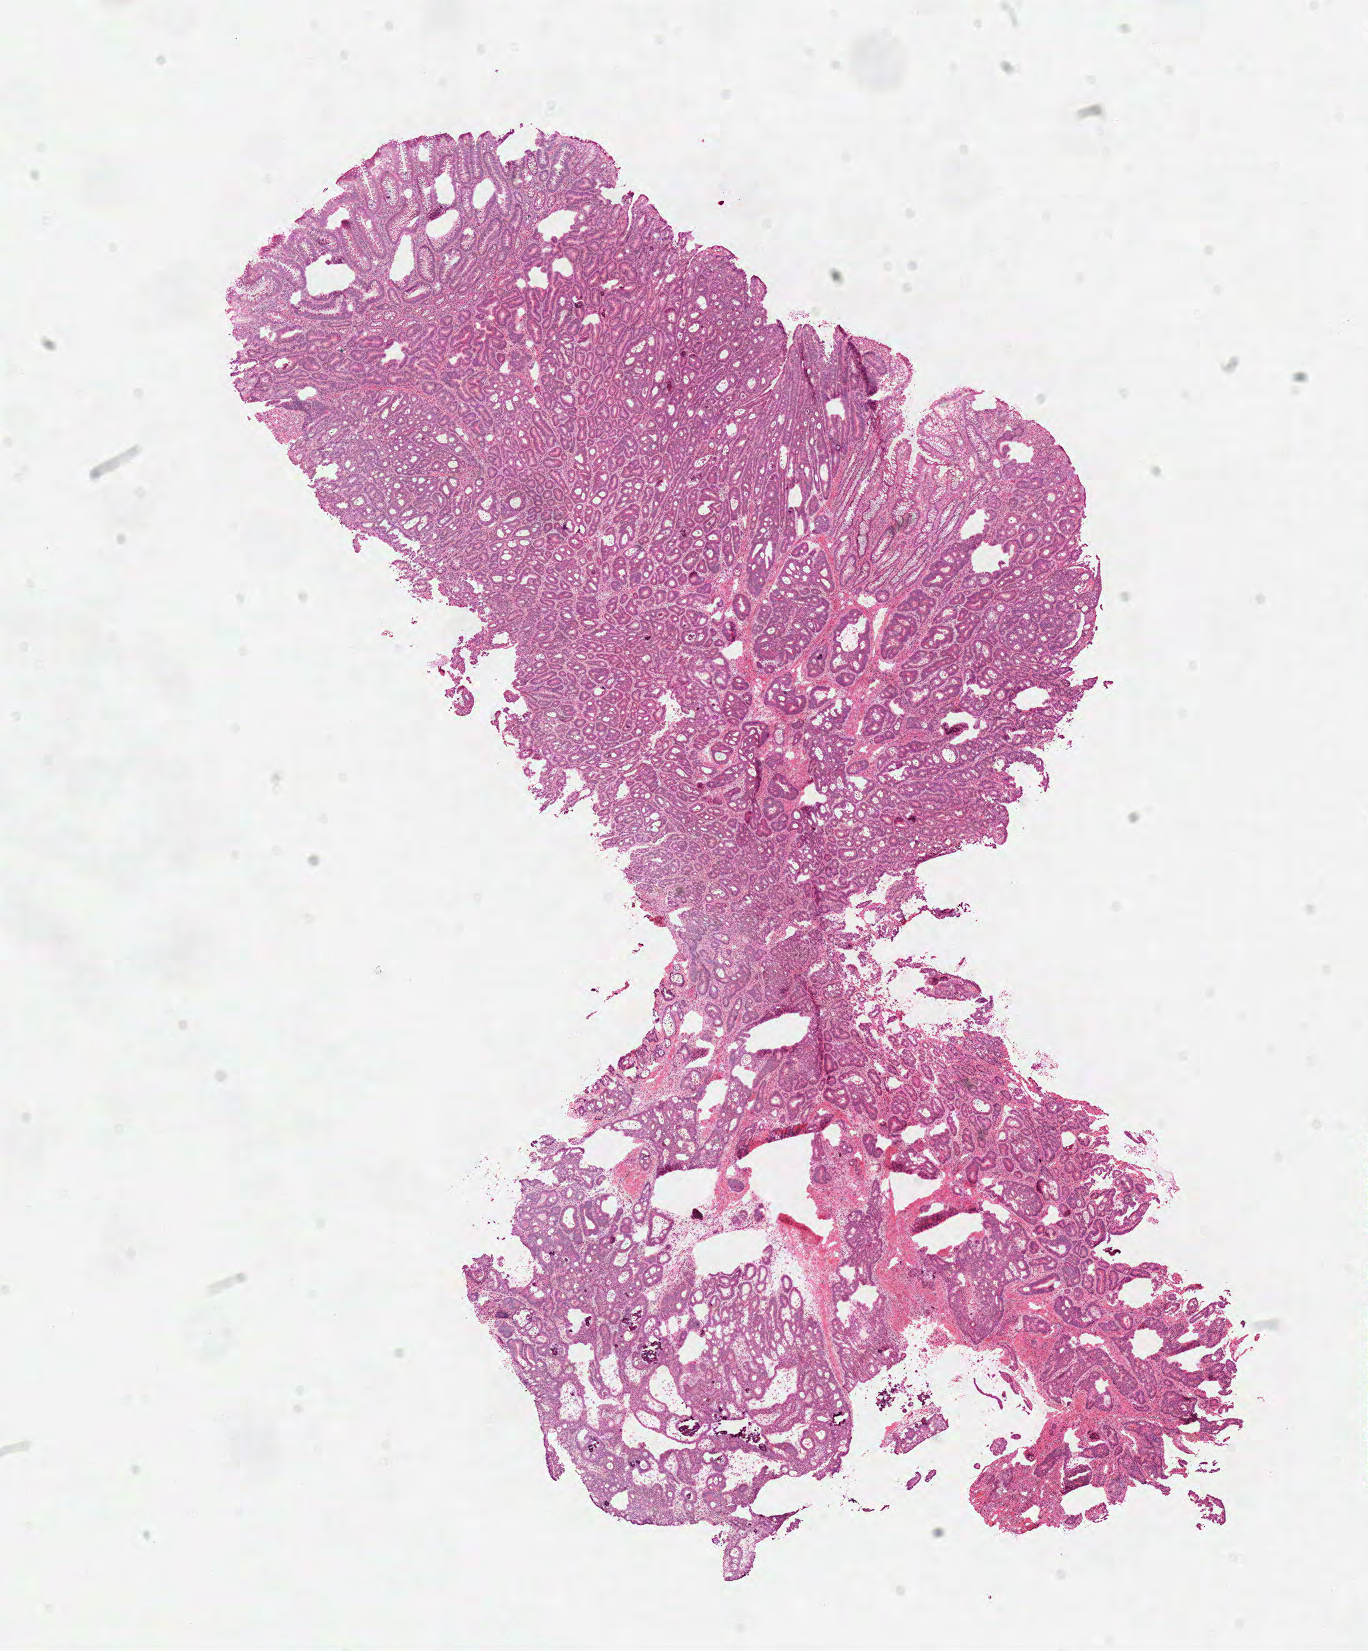
H&E whole-slide image, shown as a low-resolution overview of the whole scanned area (about 10.8 x 13.0 mm, slide scanned at 40x), frozen section from the top of the tissue portion, sample: primary tumour, colon. Female, age 70 years at initial diagnosis. Pathologist review of this section (percent, as recorded): tumour cells 68%, tumour nuclei 80%, normal cells 18%, stromal cells 10%, necrosis 5%.
Pathologic diagnosis: Adenocarcinoma, NOS (sigmoid colon). Lymph nodes positive (case pathology): 1 of 17 examined. AJCC pathologic stage: IIIB. TNM: T3 N1a M0.